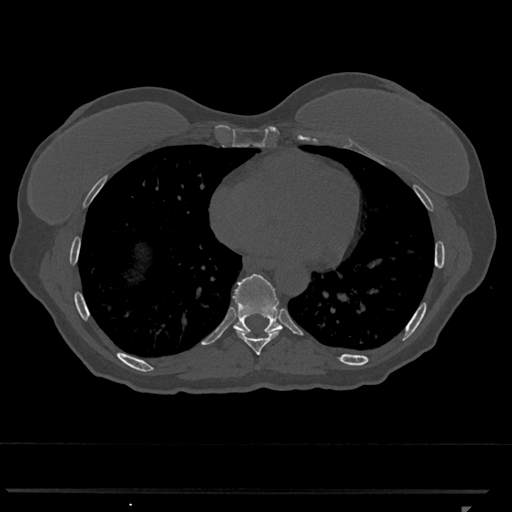
CT including the spine, one axial slice; slice 644 of 793 in the series (ordered by position); 120 kVp; bone window (W 1800 / L 400 HU); 512 × 512 image matrix, field of view 380 × 380 mm. Patient: female, 62 years. Case-level facts recorded for this patient, not image findings: primary cancer: renal.
Outlined on this slice (semi-automatically segmented with operator editing):
- T8 vertebra: box from (x=236, y=331) to (x=279, y=355) px
- T9 vertebra: (x=233, y=274)–(x=283, y=334)